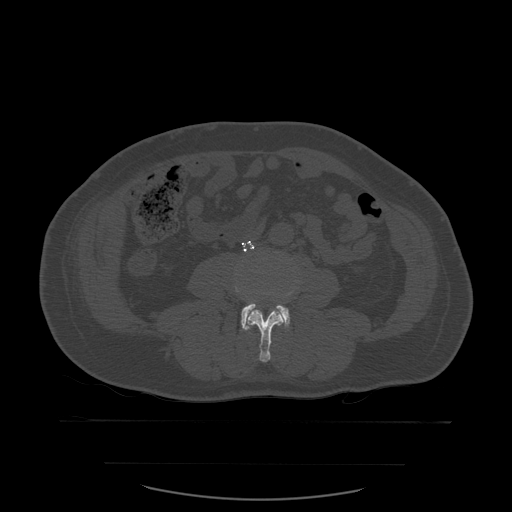
CT including the spine, one axial slice. Position 181 of 590 along the scan axis. Bone window (W 1800 / L 400 HU). 1.25 mm slice thickness. 512 × 512 image matrix. Patient age 71 years. Case-level facts recorded for this patient, not image findings: primary cancer: lung; vertebrae with lytic lesions (as recorded): T1, T2, L5, S1.
Outlined on this slice (semi-automatically segmented with operator editing):
- L3 vertebra: bounding box [x1, y1, x2, y2] px = [237, 280, 300, 363]
- L4 vertebra: [241, 303, 290, 330]